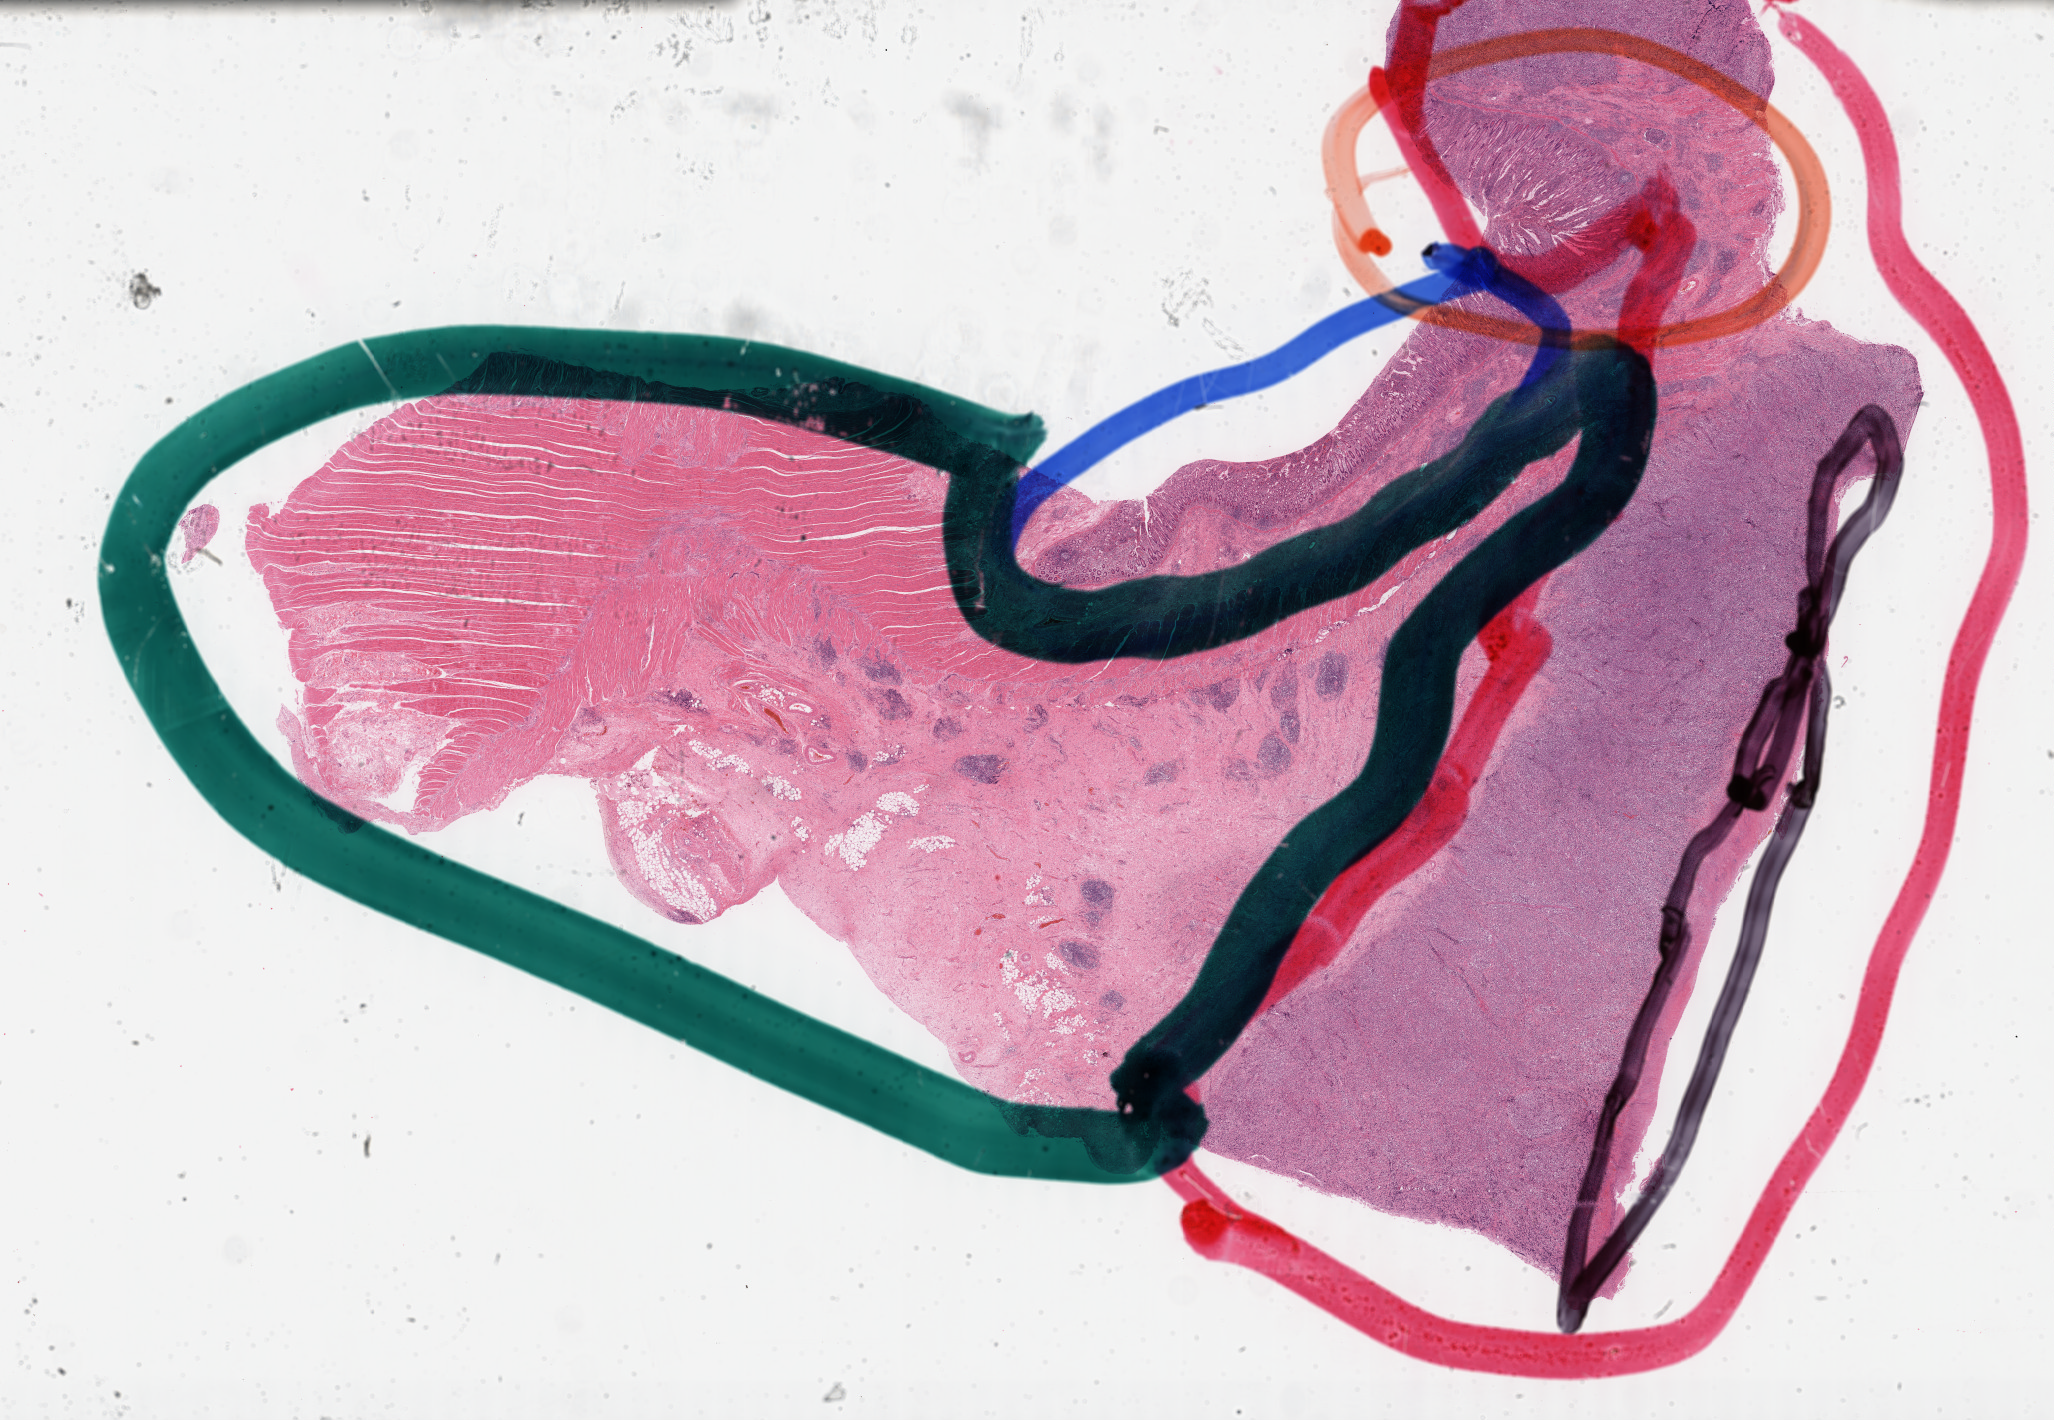
H&E-stained whole-slide image — a low-resolution overview of the entire scanned area, about 33.2 x 23.0 mm, FFPE section, lymphoid tissue, primary tumour sample. Female, age 48 years at initial diagnosis.
• diagnosis: Diffuse large B-cell lymphoma, NOS (small intestine, NOS)